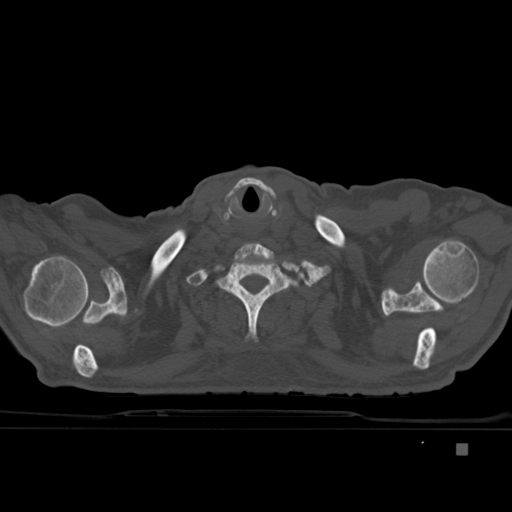
CT including the spine, one axial slice; position 359 of 451 along the scan axis; bone window (W 1800 / L 400 HU); 512 × 512 image matrix, field of view 378 × 378 mm. Male patient, age 75 years. Case-level facts recorded for this patient, not image findings: primary cancer: prostate.
Structures marked on this image (semi-automatically segmented with operator editing):
- T1 vertebra: bounding box (x1, y1, x2, y2) in pixels: (203, 255, 301, 342)